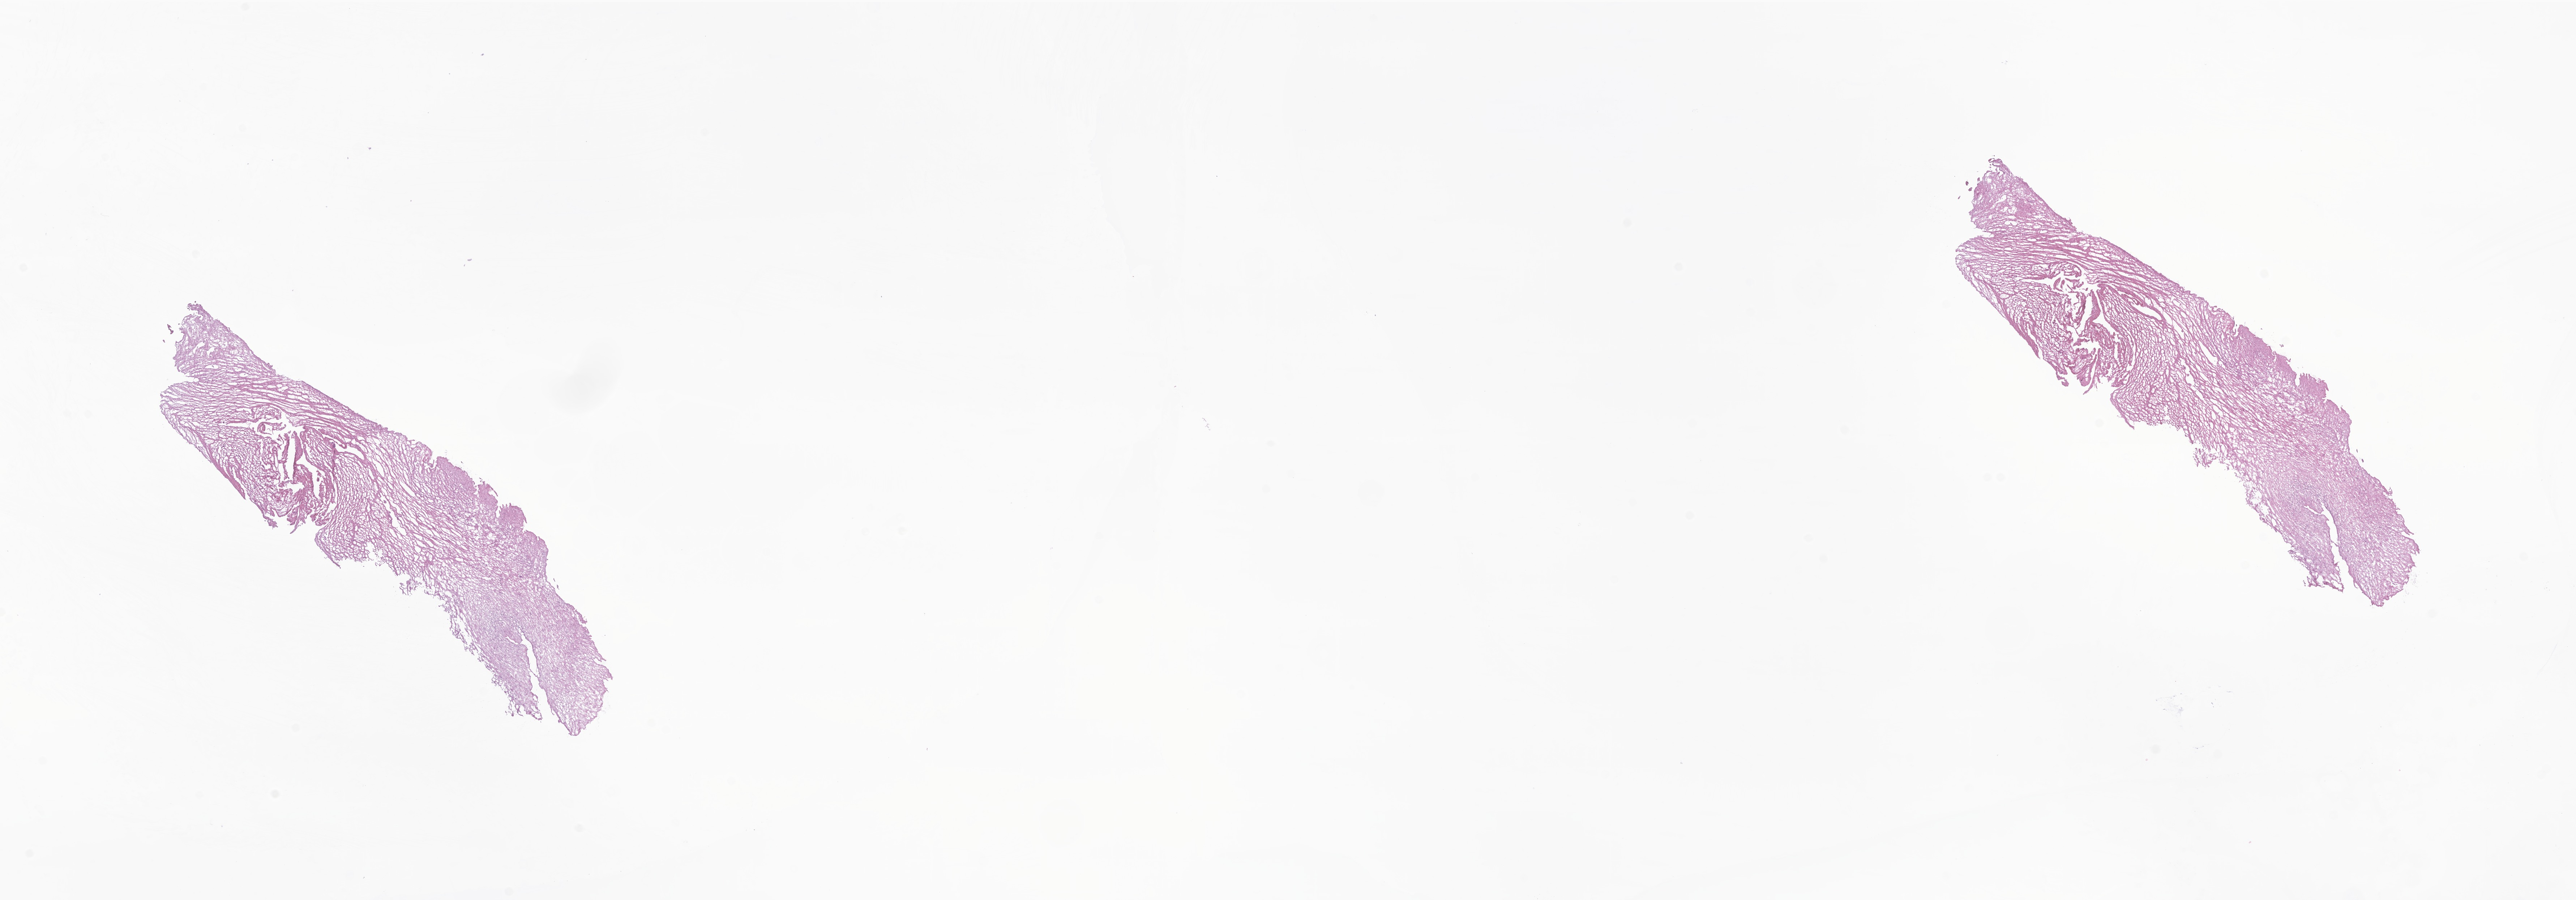
Digitized hematoxylin and eosin (H&E)-stained section of tumor tissue from the brain — low-resolution overview of the scanned area, about 30.0 x 10.5 mm, cryosection (OCT / tissue freezing medium). Patient female; age 865 days (about 2.4 years).
* diagnosis (ICD-O-3 morphology term): Glioma, malignant